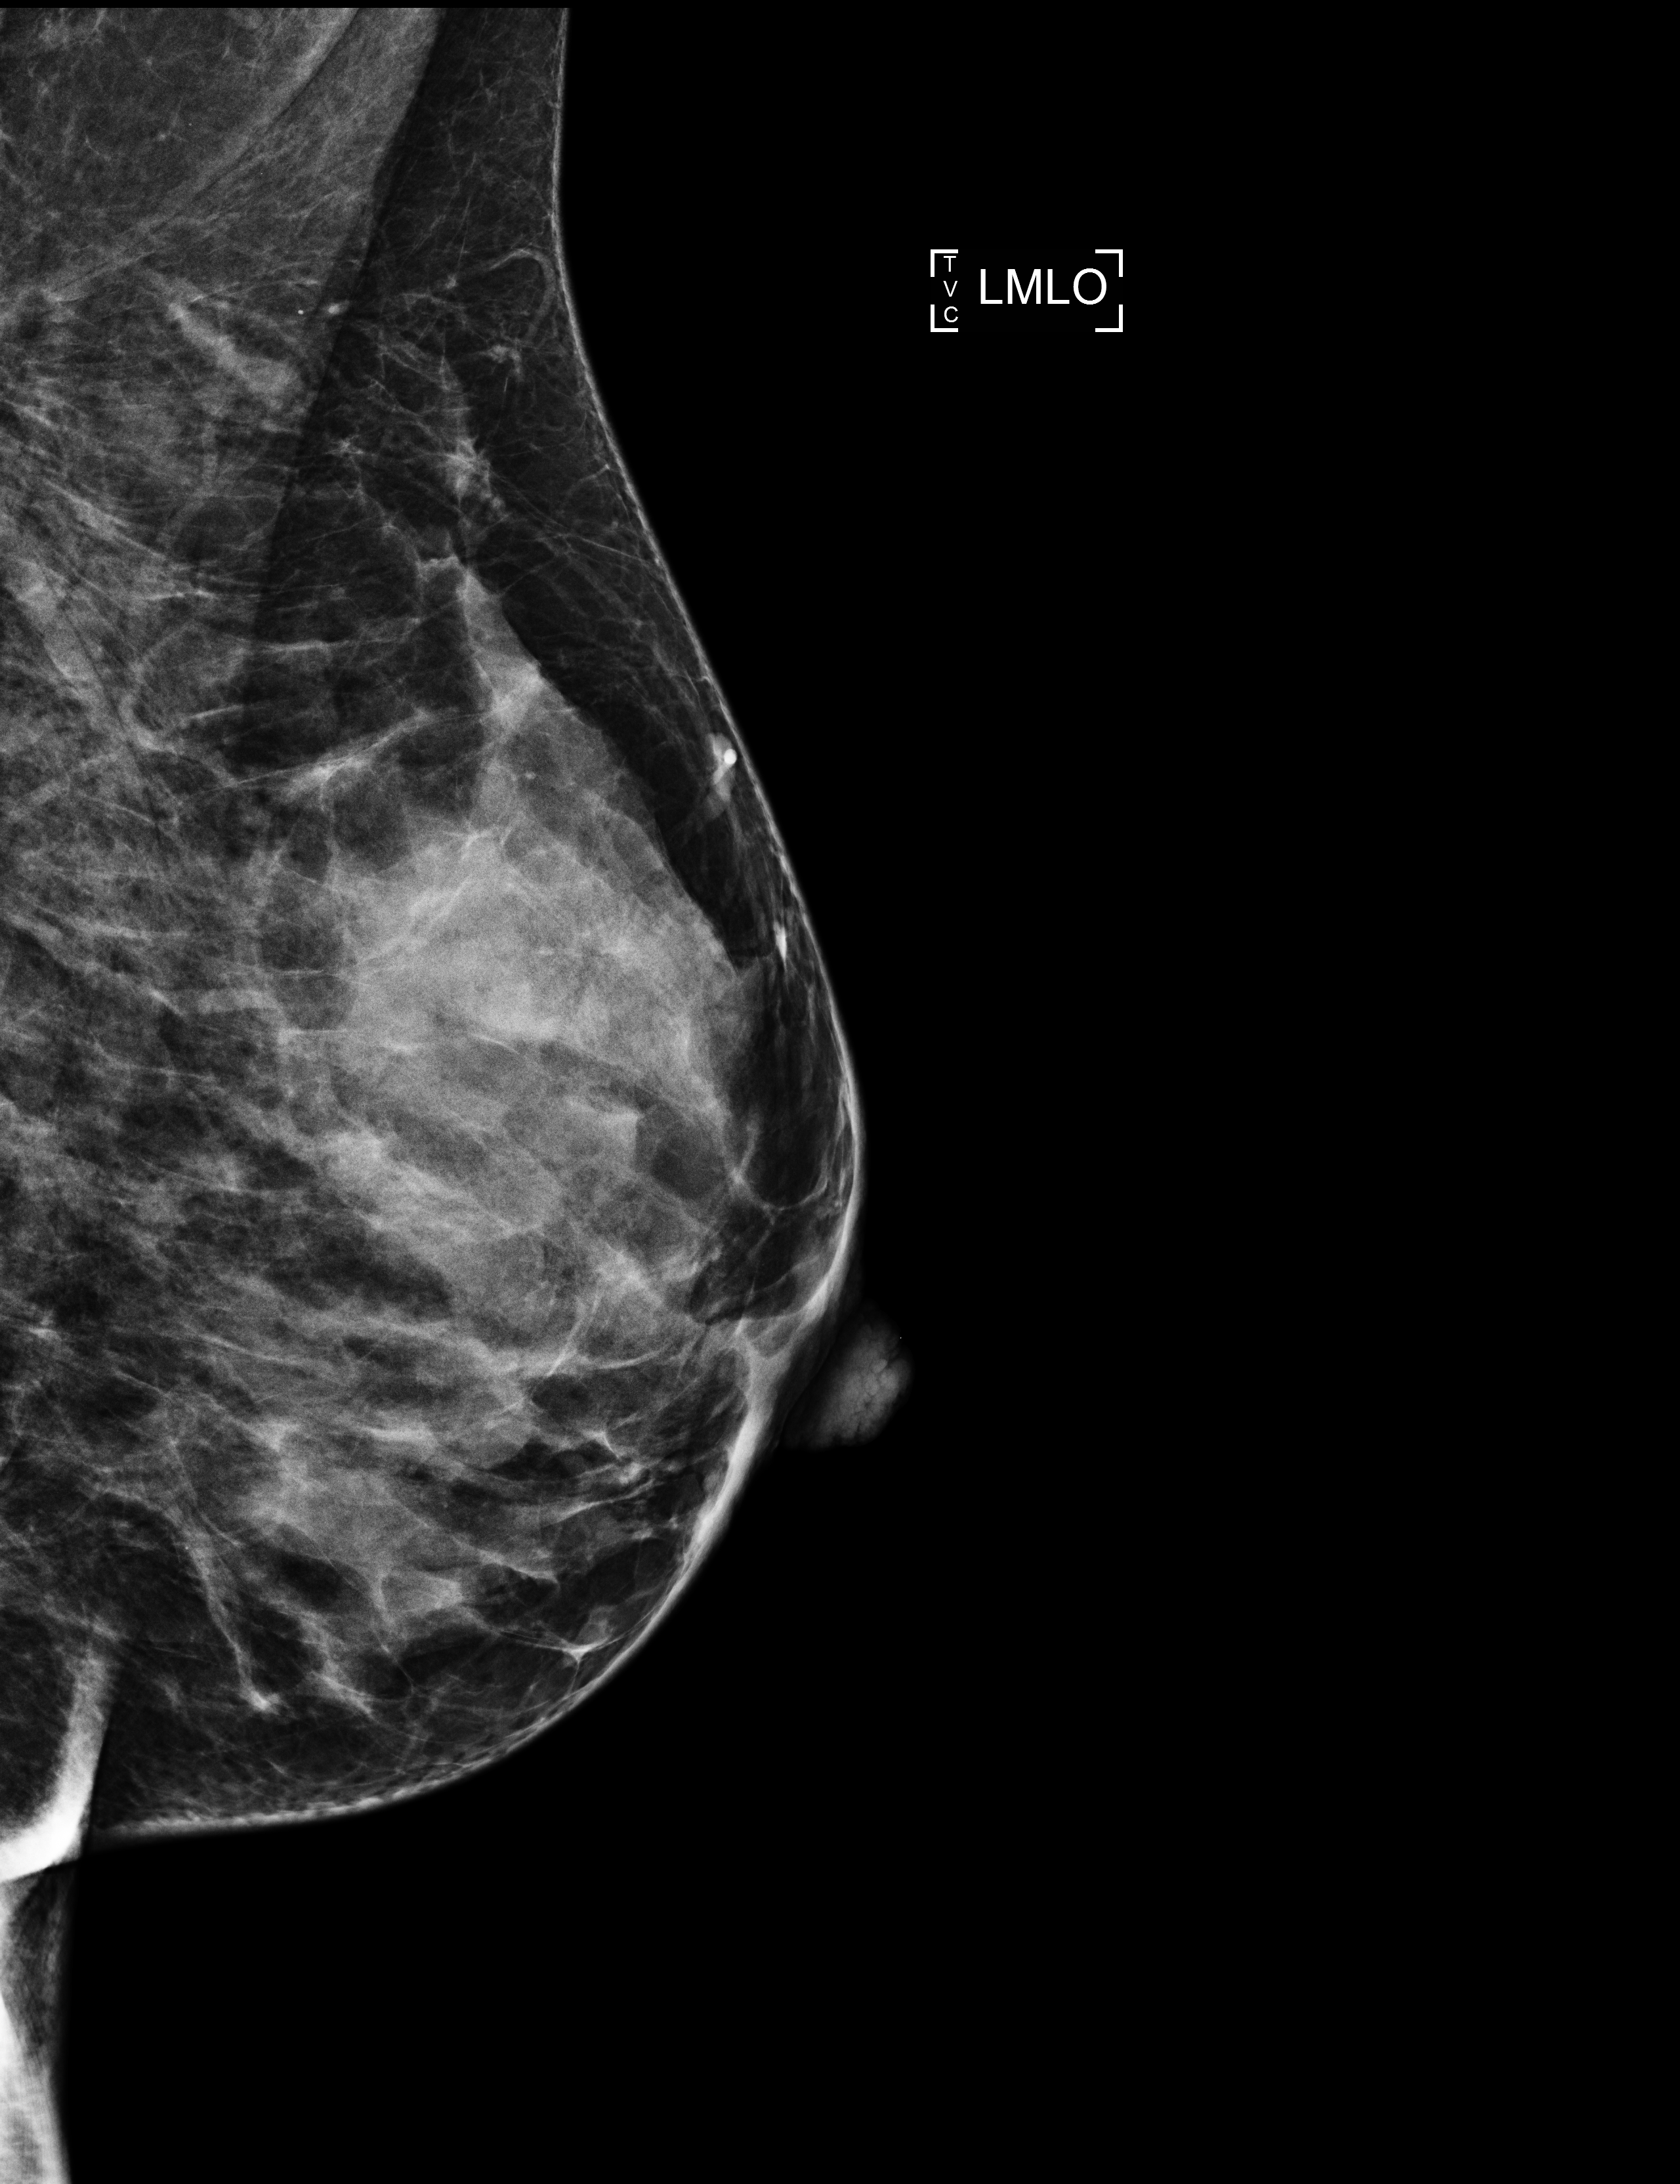
Screening examination. Patient: female, 50 years.
Image type: full-field digital mammogram. Breast: left. Projection: medio-lateral oblique projection.